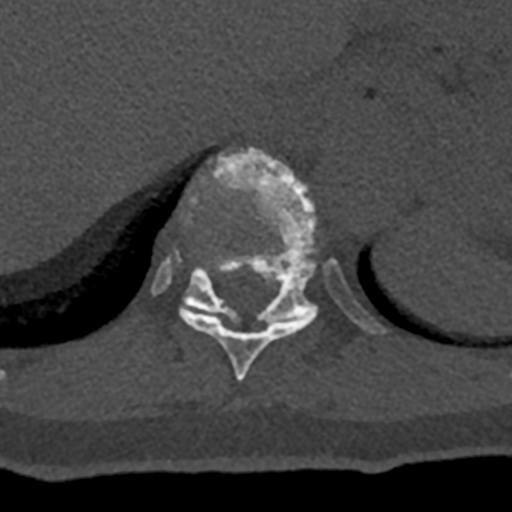
CT including the spine, one axial slice. Position 580 of 797 along the scan axis. 120 kVp. Bone window (W 1800 / L 400 HU). 0.5 mm slice thickness. 512 × 512 image matrix. Patient: male, 74 years. From the clinical record (not read from this slice): primary cancer: renal; vertebrae with lytic lesions (as recorded): T10, L1, L2, L3, L4, L5.
Annotated regions visible in this slice (semi-automatically segmented with operator editing):
- T10 vertebra: bounding box [x1, y1, x2, y2] px = [179, 152, 315, 381]
- T11 vertebra: [152, 148, 386, 334]